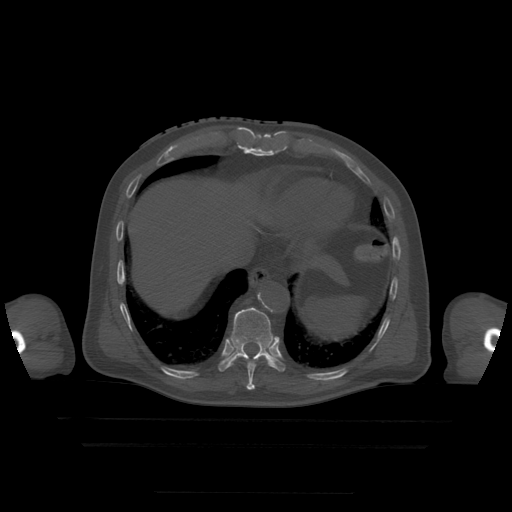
CT including the spine, one axial slice; slice 248 of 522 in the series (ordered by position); bone window (W 1800 / L 400 HU); 1.25 mm slice thickness; 512 × 512 image matrix, field of view 436 × 436 mm. Patient age 68 years. From the clinical record (not read from this slice): primary cancer: urothelial.
Outlined on this slice (semi-automatic segmentation, software-assisted and operator-edited):
- T10 vertebra: bounding box (x1, y1, x2, y2) in pixels: (218, 308, 286, 372)
- T9 vertebra: (247, 359, 258, 391)